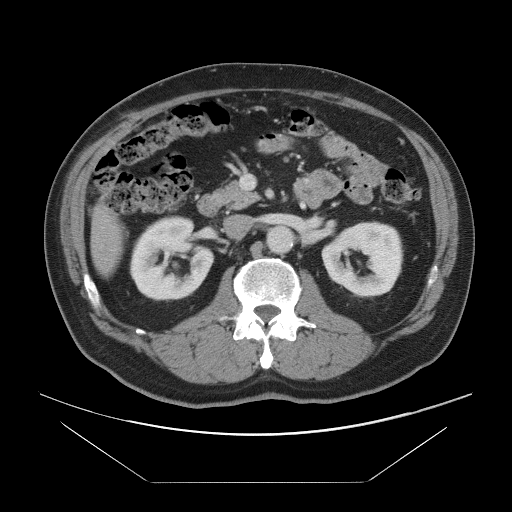
Contrast-enhanced abdominal CT, one axial slice; slice 37 of 97 in the series (ordered by position); soft-tissue window (W 400 / L 40 HU); 512 × 512 image matrix, field of view 442 × 442 mm. Male patient, age 62 years. From the clinical record (not read from this slice): diagnosis: colorectal cancer liver metastases, imaged before liver resection; multiple liver metastases: no; largest metastasis: 7 cm; disease in both lobes: yes.
Annotated regions visible in this slice (manually delineated by an expert):
- liver: bounding box [x1, y1, x2, y2] px = [93, 207, 121, 274]
- planned liver remnant (the part of the liver to remain after resection): [93, 207, 122, 274]